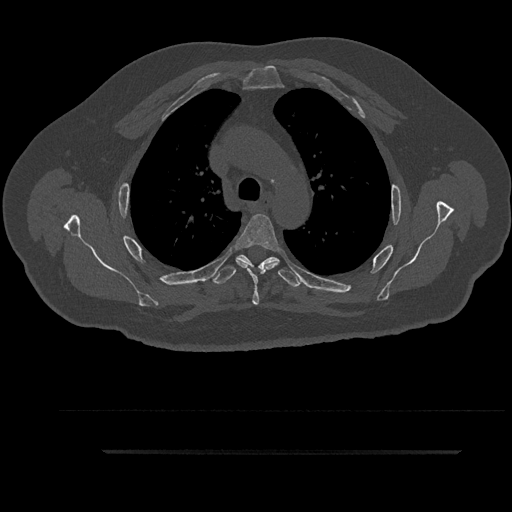
CT including the spine, one axial slice. Slice 657 of 797 in the series (ordered by position). 120 kVp. Bone window (W 1800 / L 400 HU). 0.5 mm slice thickness. 512 × 512 image matrix. Patient: male, 63 years. From the clinical record (not read from this slice): primary cancer: renal.
Outlined on this slice (semi-automatic segmentation, software-assisted and operator-edited):
- T3 vertebra: box from (x=296, y=275) to (x=299, y=278) px
- T4 vertebra: (x=236, y=214)–(x=280, y=305)
- T5 vertebra: (x=213, y=254)–(x=301, y=288)